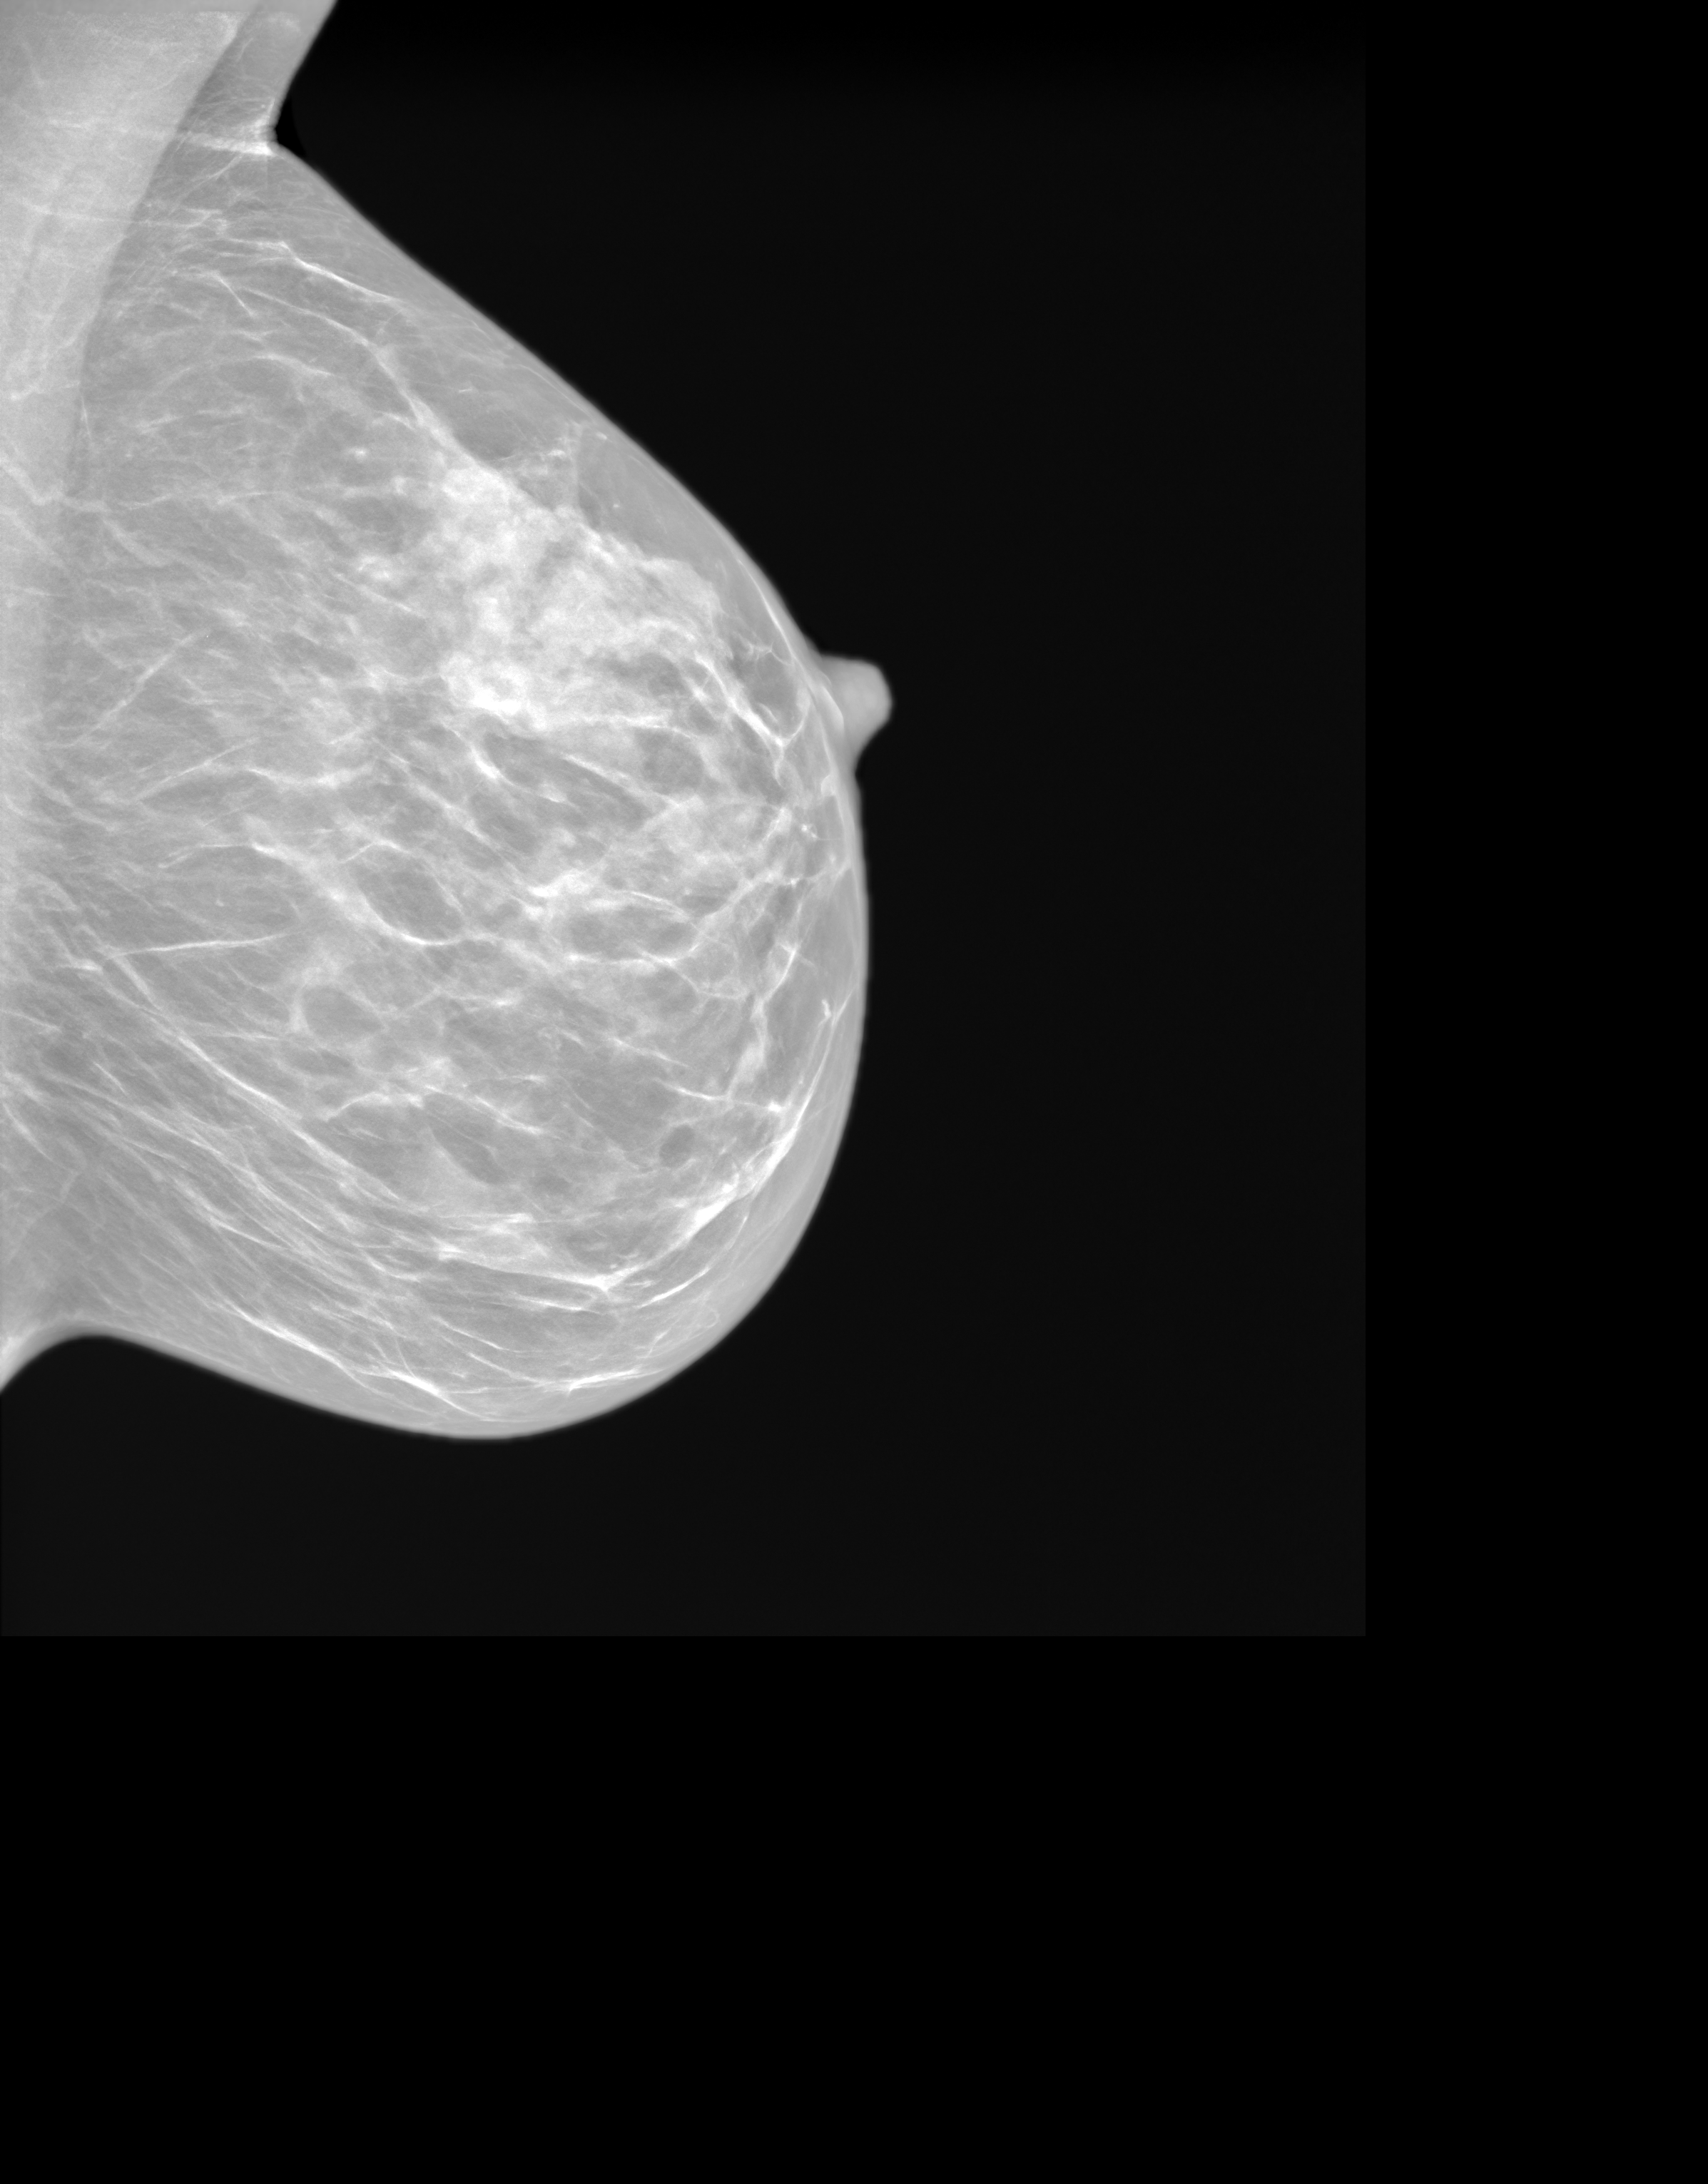
Synthetic 2-D view generated from a tomosynthesis acquisition (not an FFDM exposure); left breast; mediolateral oblique (MLO) view; annual screening mammography examination. Patient aged 56 years (female).
- breast density at the screening exam (both breasts): heterogeneously dense (BI-RADS density category c)
- final BI-RADS assessment for this screening round (tomosynthesis exam, both breasts): category 1
- recall: no recall after this screen